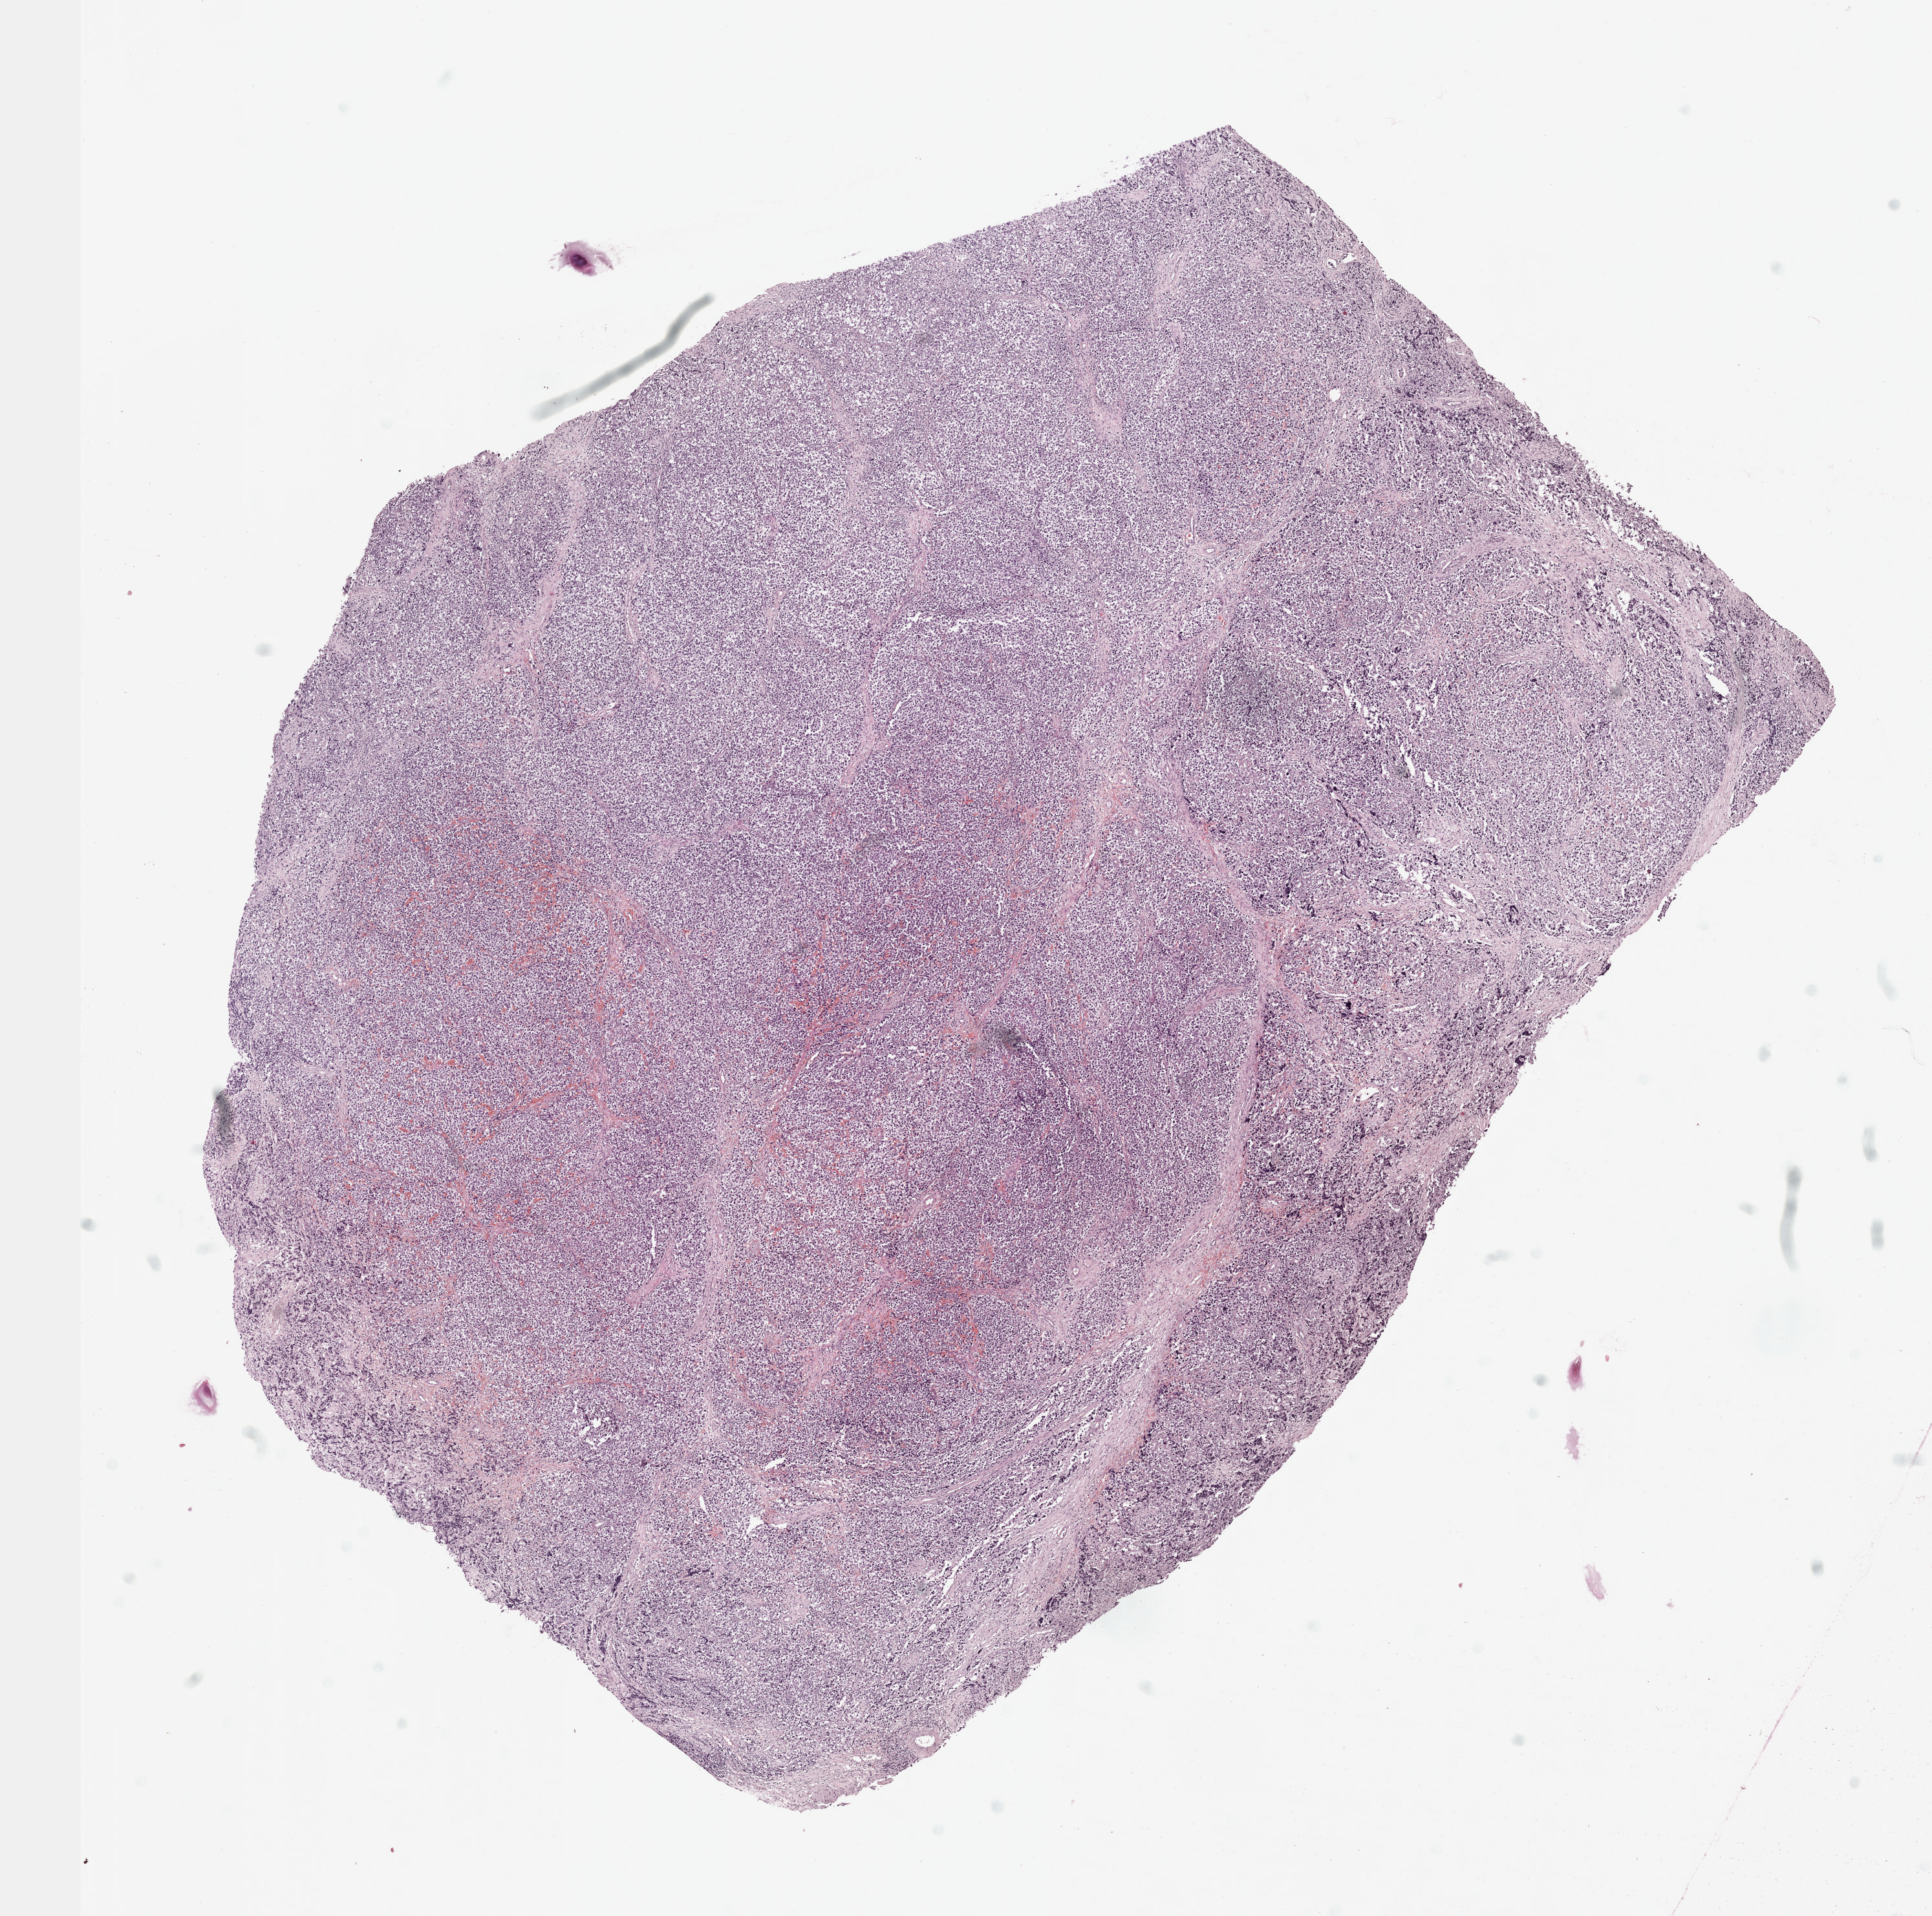
H&E whole-slide image — a low-resolution overview of the entire scanned area, about 12.1 x 12.0 mm (acquisition: 40x scan). Formalin-fixed paraffin-embedded (FFPE) diagnostic section. Primary tumour sample from the testis. Patient: male, age at initial diagnosis 31 years.
AJCC pathologic stage: IS. Laterality: right. Histologic diagnosis: Seminoma, NOS.